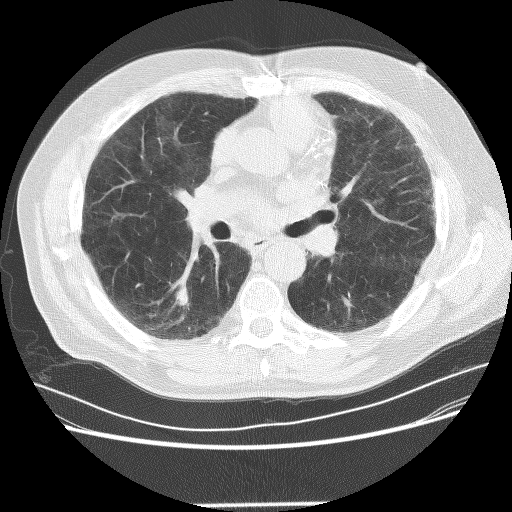
Axial slice from a low-dose chest CT screening exam. Baseline annual screen. Lung window (W 1500 / L -600 HU). 2.5 mm slice thickness. 120 kVp. Slice 123 of 281 in the series. Male, age 72 years at enrolment.
Expert-annotated lung lesion, box from (x=157, y=279) to (x=201, y=322) px. The screening reader recorded 2 non-calcified nodules or masses ≥4 mm on this exam (right lower lobe, left lower lobe); which of them this box marks is not recorded. Lung cancer was diagnosed 436 days after this screen: squamous cell carcinoma, NOS, right lower lobe, poorly differentiated (G3), stage IB (AJCC 6th edition), 42 mm at pathology.